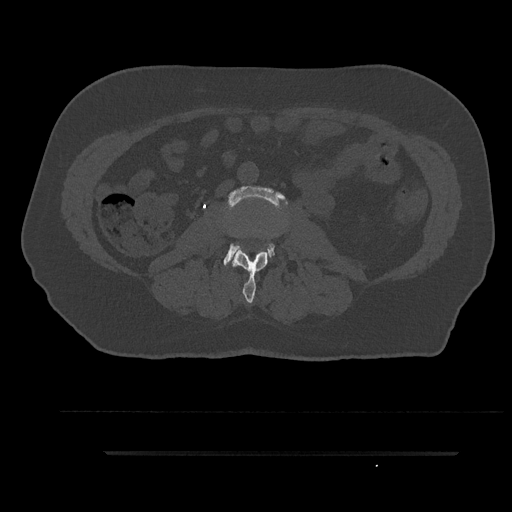
CT including the spine, one axial slice; reconstruction kernel Br40s/3; 120 kVp; bone window (W 1800 / L 400 HU); 0.5 mm slice thickness; 512 × 512 image matrix. Male patient, age 63 years. Case-level facts recorded for this patient, not image findings: primary cancer: renal; vertebrae with lytic lesions (as recorded): T8.
Outlined on this slice (semi-automatic segmentation, software-assisted and operator-edited):
- L2 vertebra: box from (x=232, y=251) to (x=268, y=303) px
- L3 vertebra: (x=224, y=185)–(x=285, y=266)